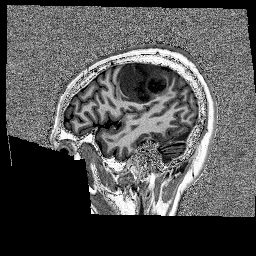
Brain MRI from a brain-tumour surgery series, one sagittal slice. Position 43 of 176 along the scan axis. 1 mm slice thickness. 256 × 256 image matrix, field of view 256 × 256 mm. From the clinical record (not read from this slice): histopathology: Glioblastoma; WHO grade: 4; IDH mutation: no; tumour location: Left Frontal.
Outlined on this slice (expert manual segmentation):
- tumour: bounding box [x1, y1, x2, y2] px = [118, 61, 175, 102]